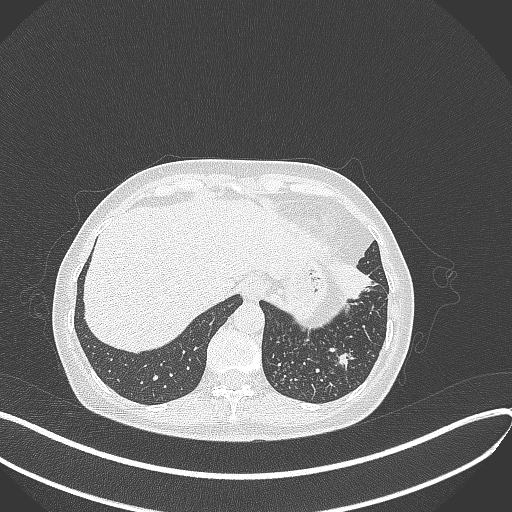
Chest CT, one axial slice; slice 79 of 429 in the series (ordered by position); reconstruction kernel B70f; 100 kVp; lung window (W 1500 / L -600 HU); 1 mm slice thickness; 512 × 512 image matrix, field of view 400 × 400 mm. Female patient, age 63 years. From the clinical record (not read from this slice): clinical TNM (as recorded): T1b N0 M0; histopathological grade: G2-3.
Structures marked on this image (bounding box drawn by a radiologist):
- lung tumour (recorded histology: adenocarcinoma): bounding box <332,260,374,305> (left, top, right, bottom; pixels)